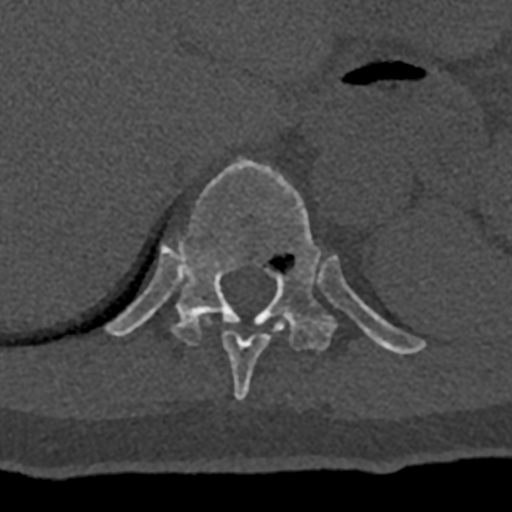
CT including the spine, one axial slice. Slice 567 of 797 in the series (ordered by position). Reconstruction kernel Br40s/3. Bone window (W 1800 / L 400 HU). 512 × 512 image matrix, field of view 160 × 160 mm. Male patient, age 74 years. From the clinical record (not read from this slice): primary cancer: renal; vertebrae with lytic lesions (as recorded): T10, L1, L2, L3, L4, L5.
Outlined on this slice (semi-automatic segmentation, software-assisted and operator-edited):
- T10 vertebra: bounding box (x1, y1, x2, y2) in pixels: (207, 319, 286, 400)
- T11 vertebra: (106, 157, 426, 354)